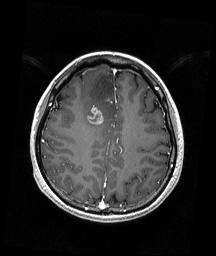
Brain MRI from a brain-tumour surgery series, one axial slice; position 61 of 192 along the scan axis; T1-weighted post-contrast; 1 mm slice thickness; 216 × 256 image matrix, field of view 211 × 250 mm. From the clinical record (not read from this slice): histopathology: Astrocytoma; WHO grade: 4; IDH mutation: yes; tumour location: Right Frontal.
Outlined on this slice (outlined manually by an expert reader):
- tumour: bounding box (x1, y1, x2, y2) in pixels: (88, 106, 104, 125)